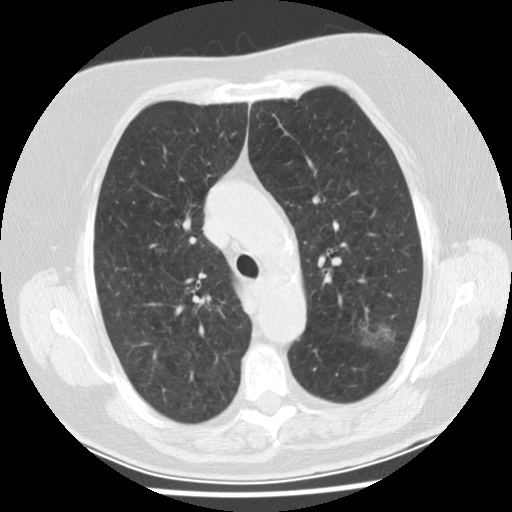
Axial slice from a low-dose chest CT screening exam. Baseline annual screen. Lung window (W 1500 / L -600 HU). Standard (soft-tissue) reconstruction kernel (STANDARD). Female, age 74 years at enrolment. Former smoker at enrolment.
• Expert reader's lesion annotation, bounding box <338,307,409,363> (left, top, right, bottom; pixels).
• The screening reader recorded 2 non-calcified nodules or masses ≥4 mm on this exam (left upper lobe, left lower lobe); which of them this box marks is not recorded.
• Participant outcome: lung cancer diagnosed 532 days after this screen — bronchiolo-alveolar adenocarcinoma, NOS, left upper lobe, stage IA (AJCC 6th edition), 20 mm at pathology.